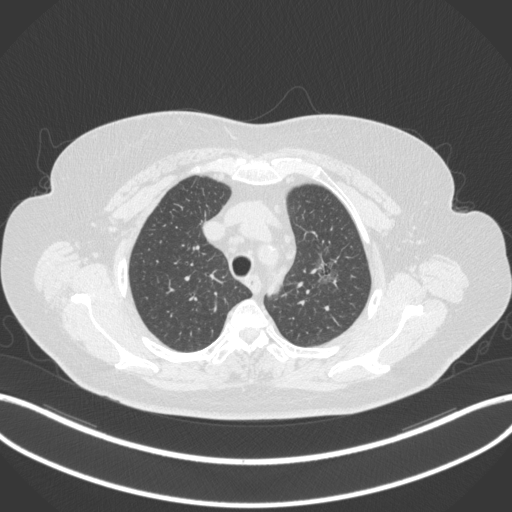
Chest CT, one axial slice. Position 267 of 310 along the scan axis. 120 kVp. Lung window (W 1500 / L -600 HU). 512 × 512 image matrix, field of view 400 × 400 mm. Female patient, age 70 years. Case-level facts recorded for this patient, not image findings: clinical TNM (as recorded): T1c N0 M0.
Annotated regions visible in this slice (bounding box drawn by a radiologist):
- lung tumour (recorded histology: adenocarcinoma): bounding box (x1, y1, x2, y2) in pixels: (311, 253, 343, 287)